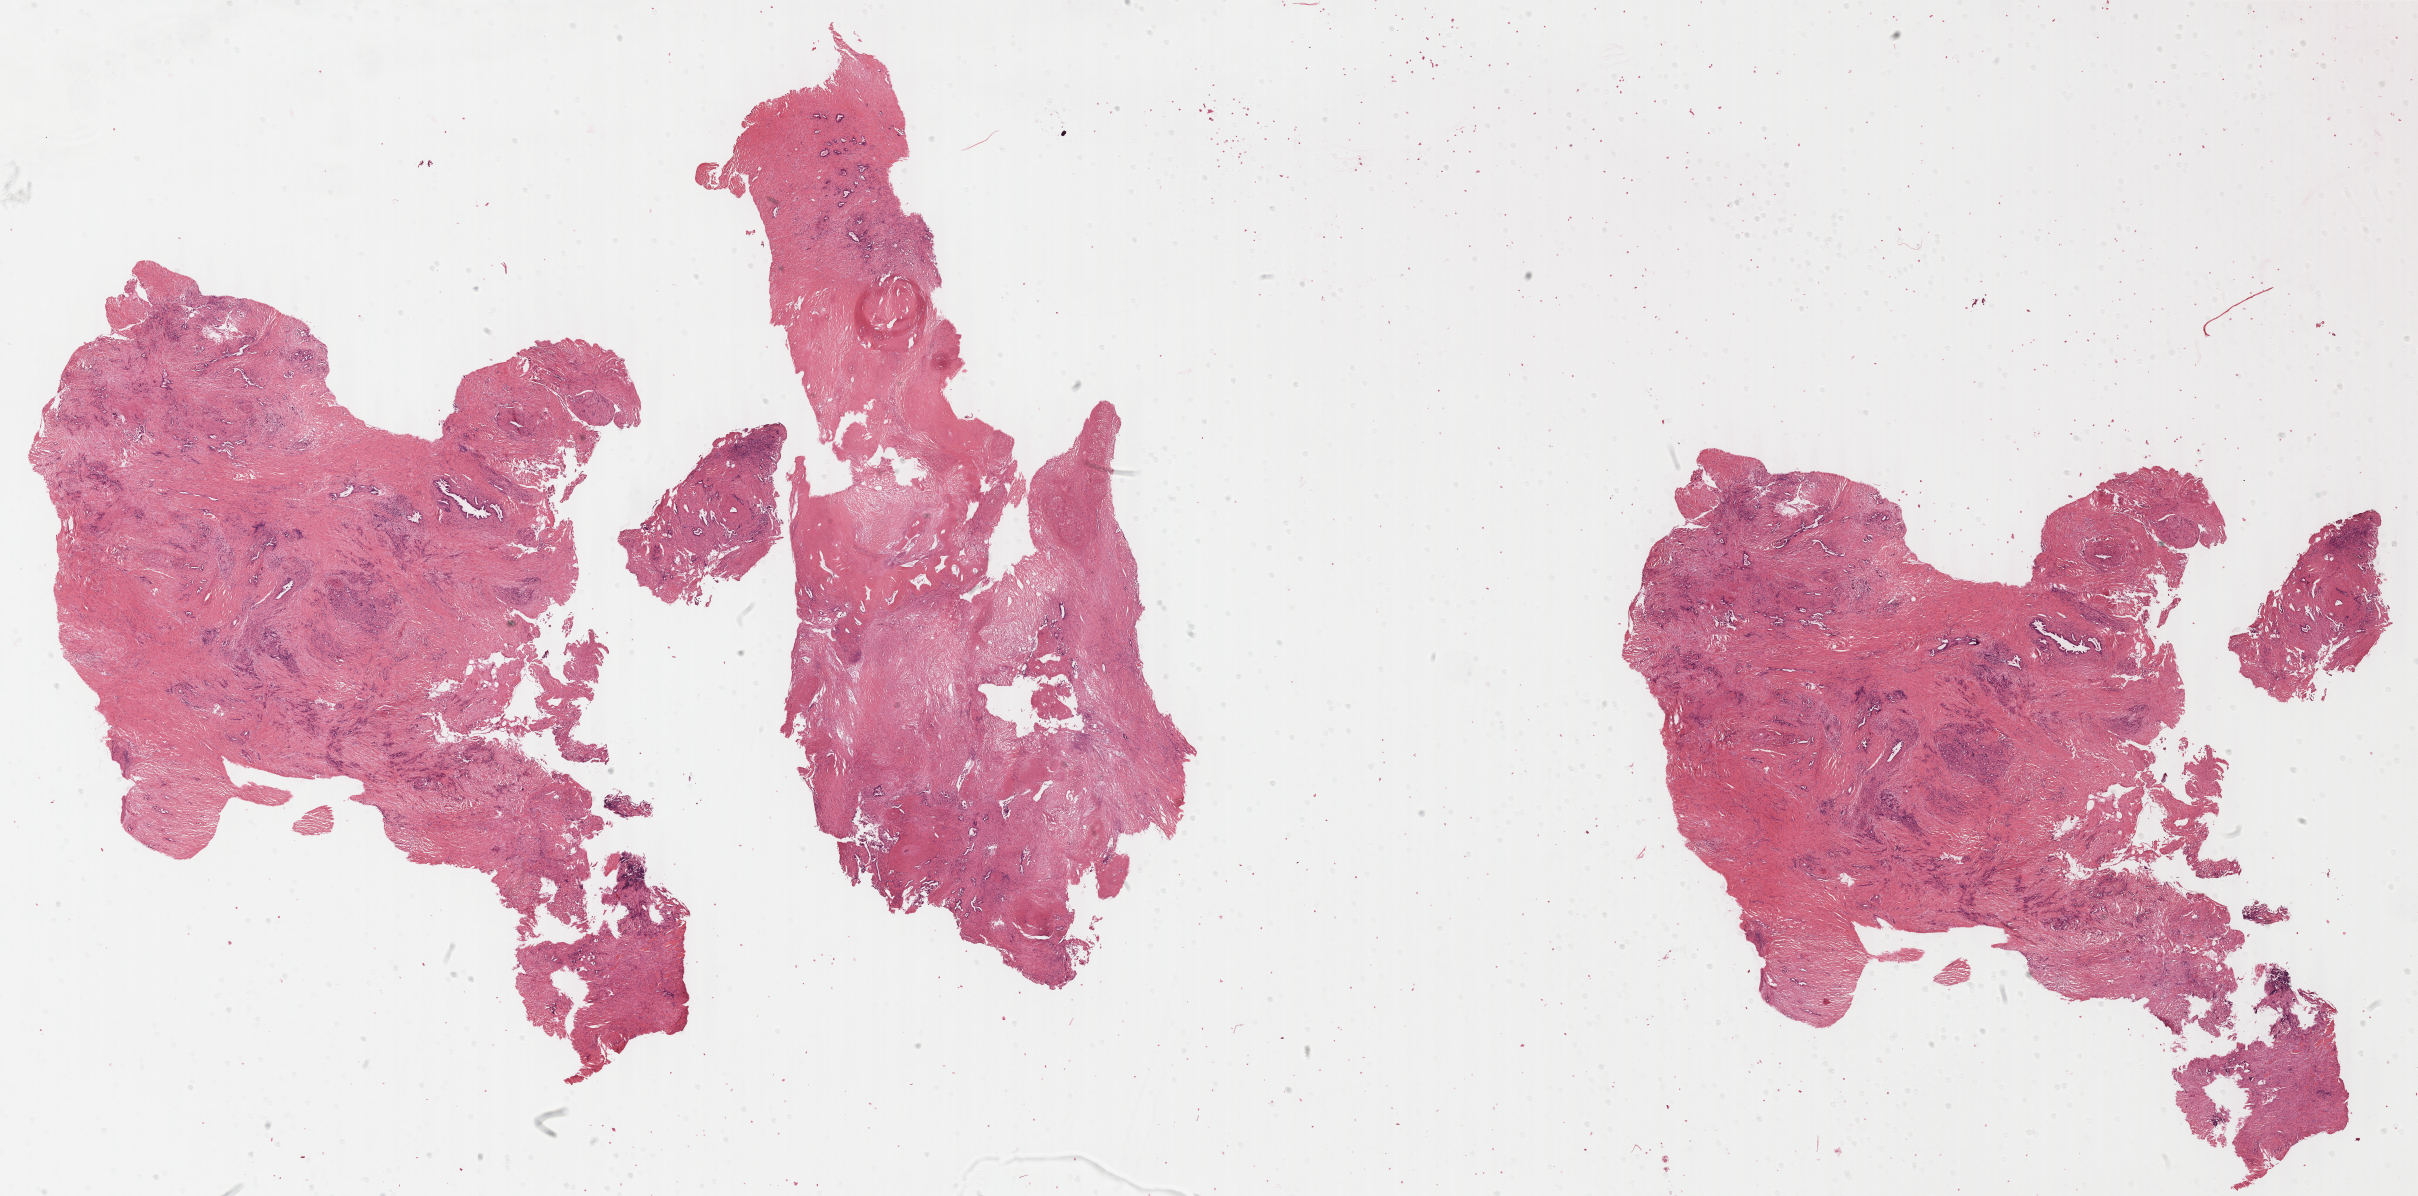
Hematoxylin and eosin (H&E) stained whole-slide image, a low-resolution overview of the entire scanned area, about 38.5 x 19.0 mm (acquisition: 40x scan); FFPE section; primary tumour sample from the pancreas. Patient: female, age at initial diagnosis 49 years. Histologic grade: G2 (moderately differentiated).
* lymph nodes positive (case pathology): 0 of 21 examined
* AJCC pathologic stage: III (7th edition)
* histologic diagnosis: Infiltrating duct carcinoma, NOS (head of pancreas)